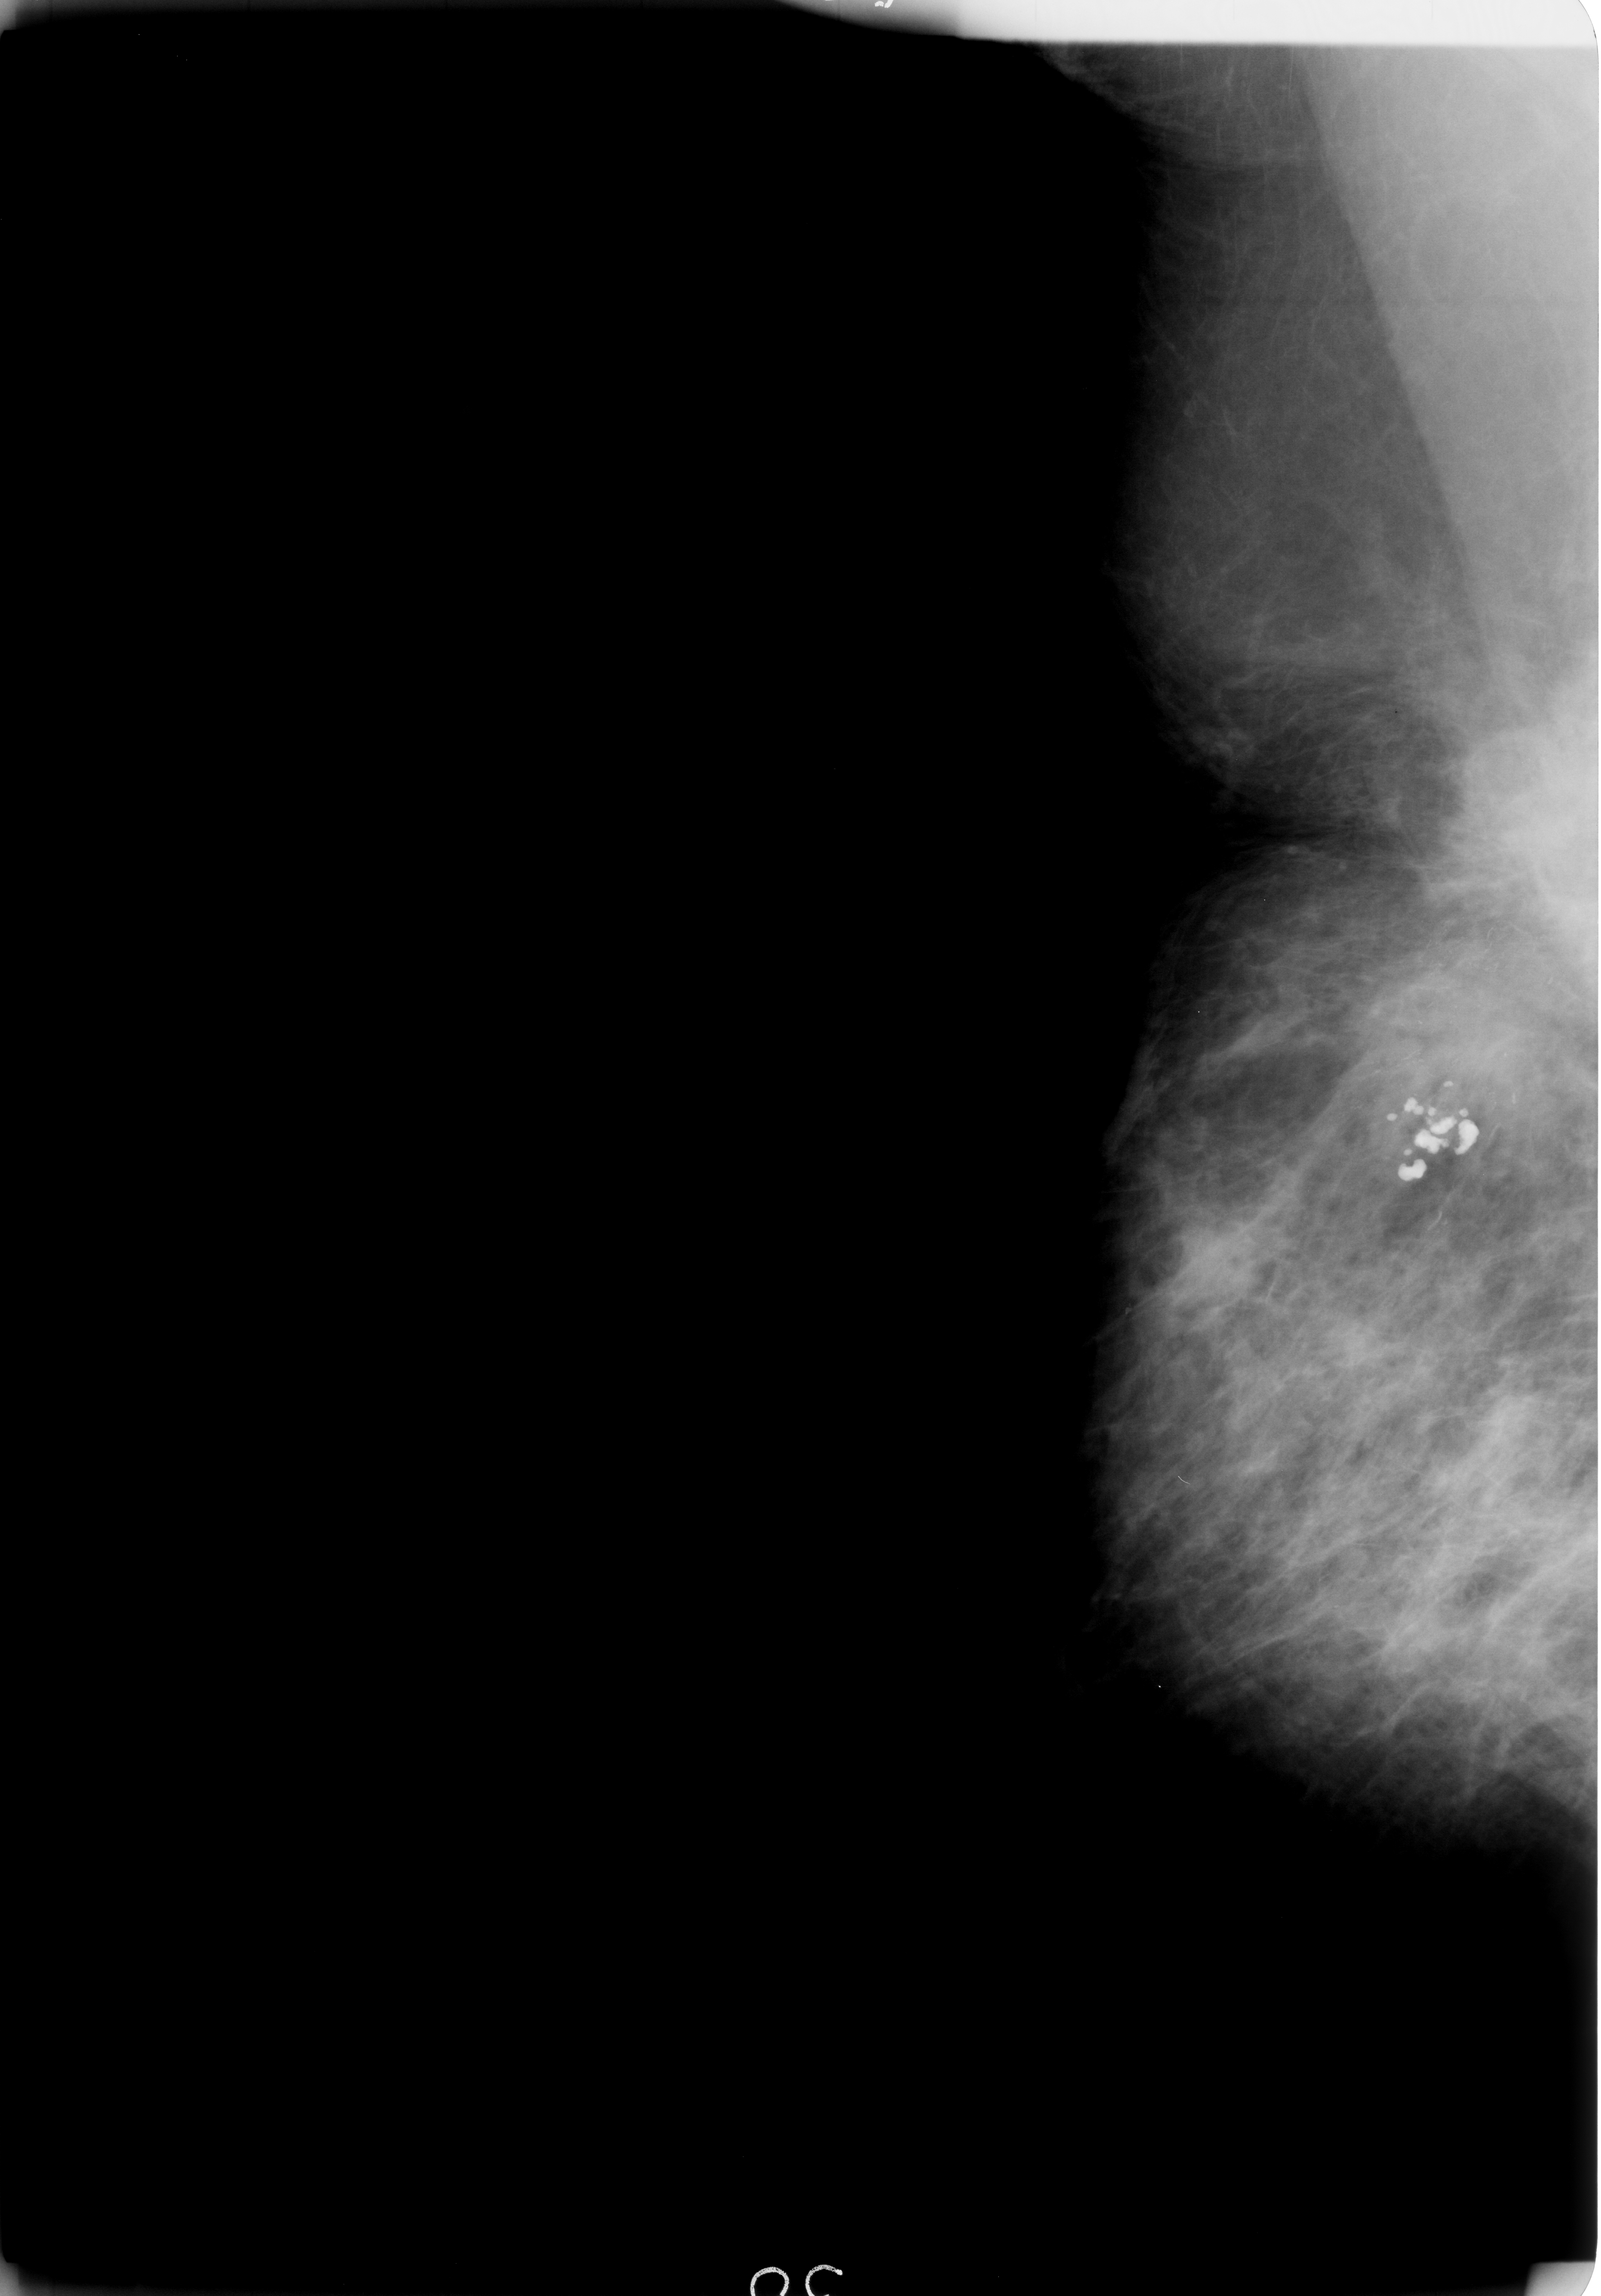
Scanned film-screen mammogram. Right breast. Mediolateral oblique (MLO) view. Breast composition: scattered fibroglandular densities (BI-RADS density category 2 of 4). 1601 × 2296 image matrix.
Expert-marked regions of interest on this image (one box per marked abnormality):
- mass, shape irregular / architectural distortion, margins ill defined / spiculated; BI-RADS assessment category 5; pathology result (as recorded, not read from the image): malignant: box from (x=1382, y=837) to (x=1601, y=1145) px